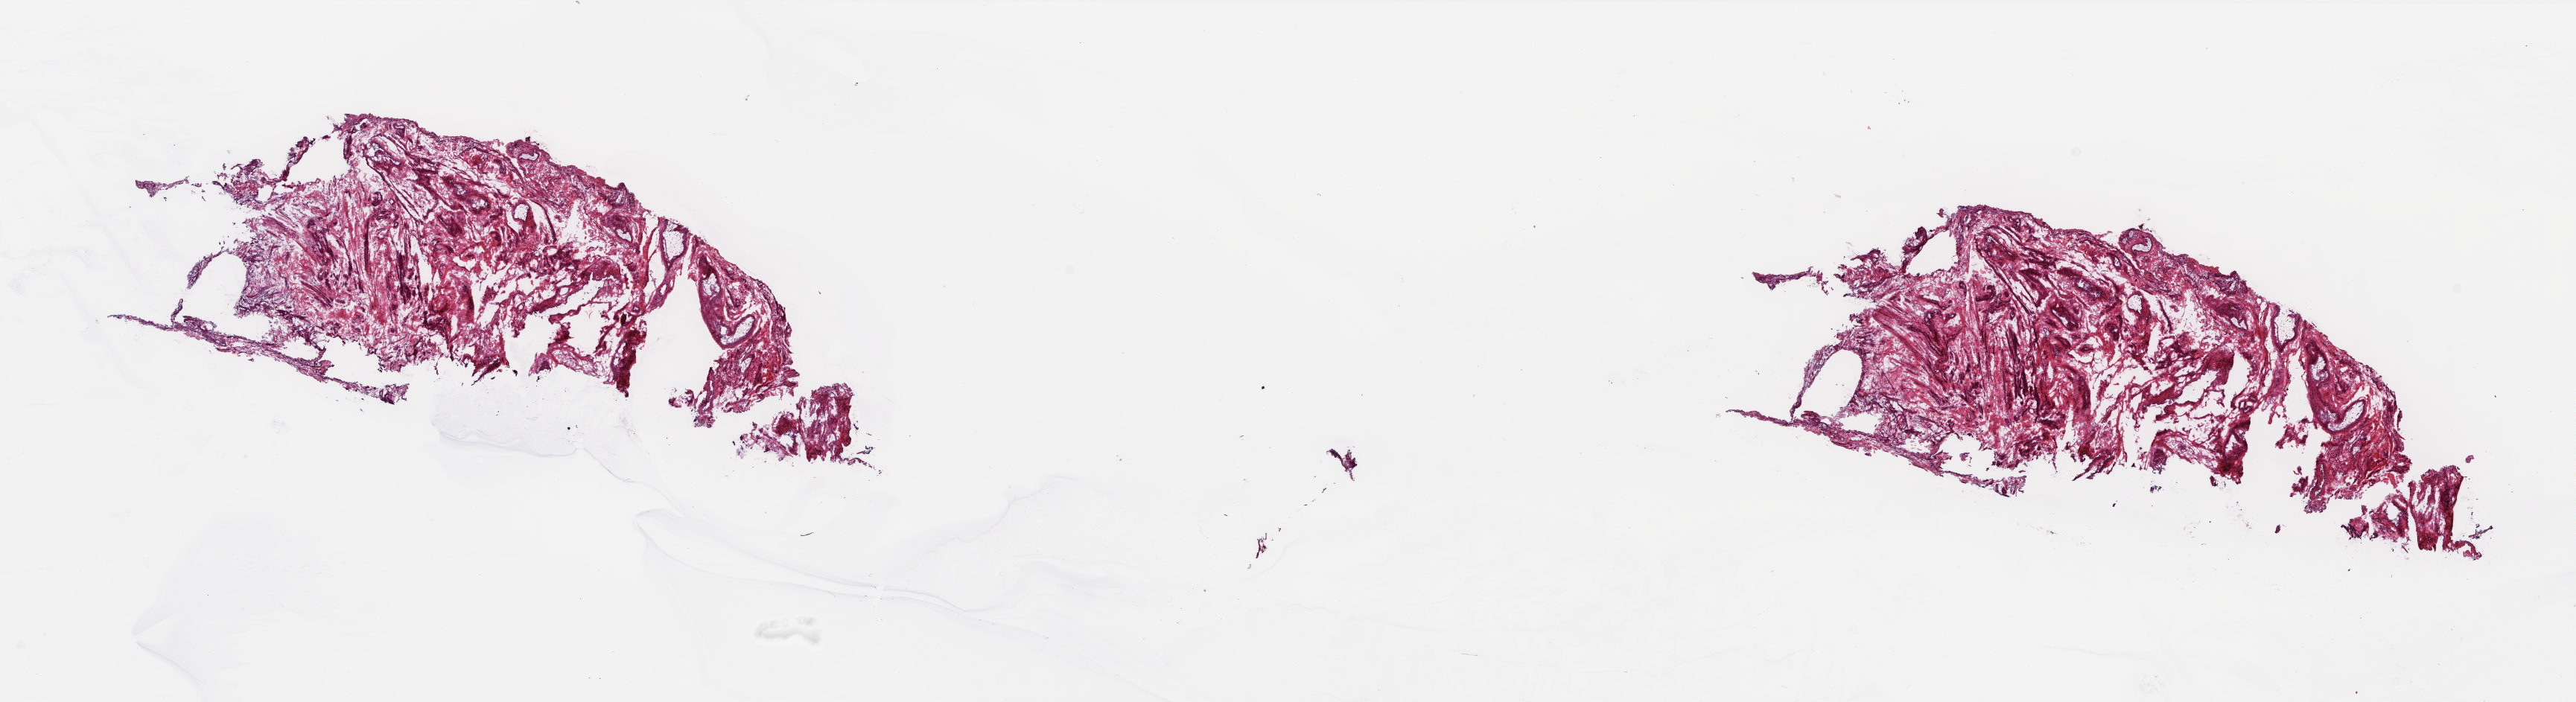
H&E-stained whole-slide image, low-resolution overview of the scanned area, about 27.9 x 7.6 mm (from a 20x scan), frozen section from the top of the tissue portion, solid tissue normal (non-tumour tissue) sample from the uterus. Female, age 84 years at initial diagnosis.
This section: solid tissue normal (non-tumour) sample from the same patient. Patient diagnosis: Mullerian mixed tumor (endometrium).